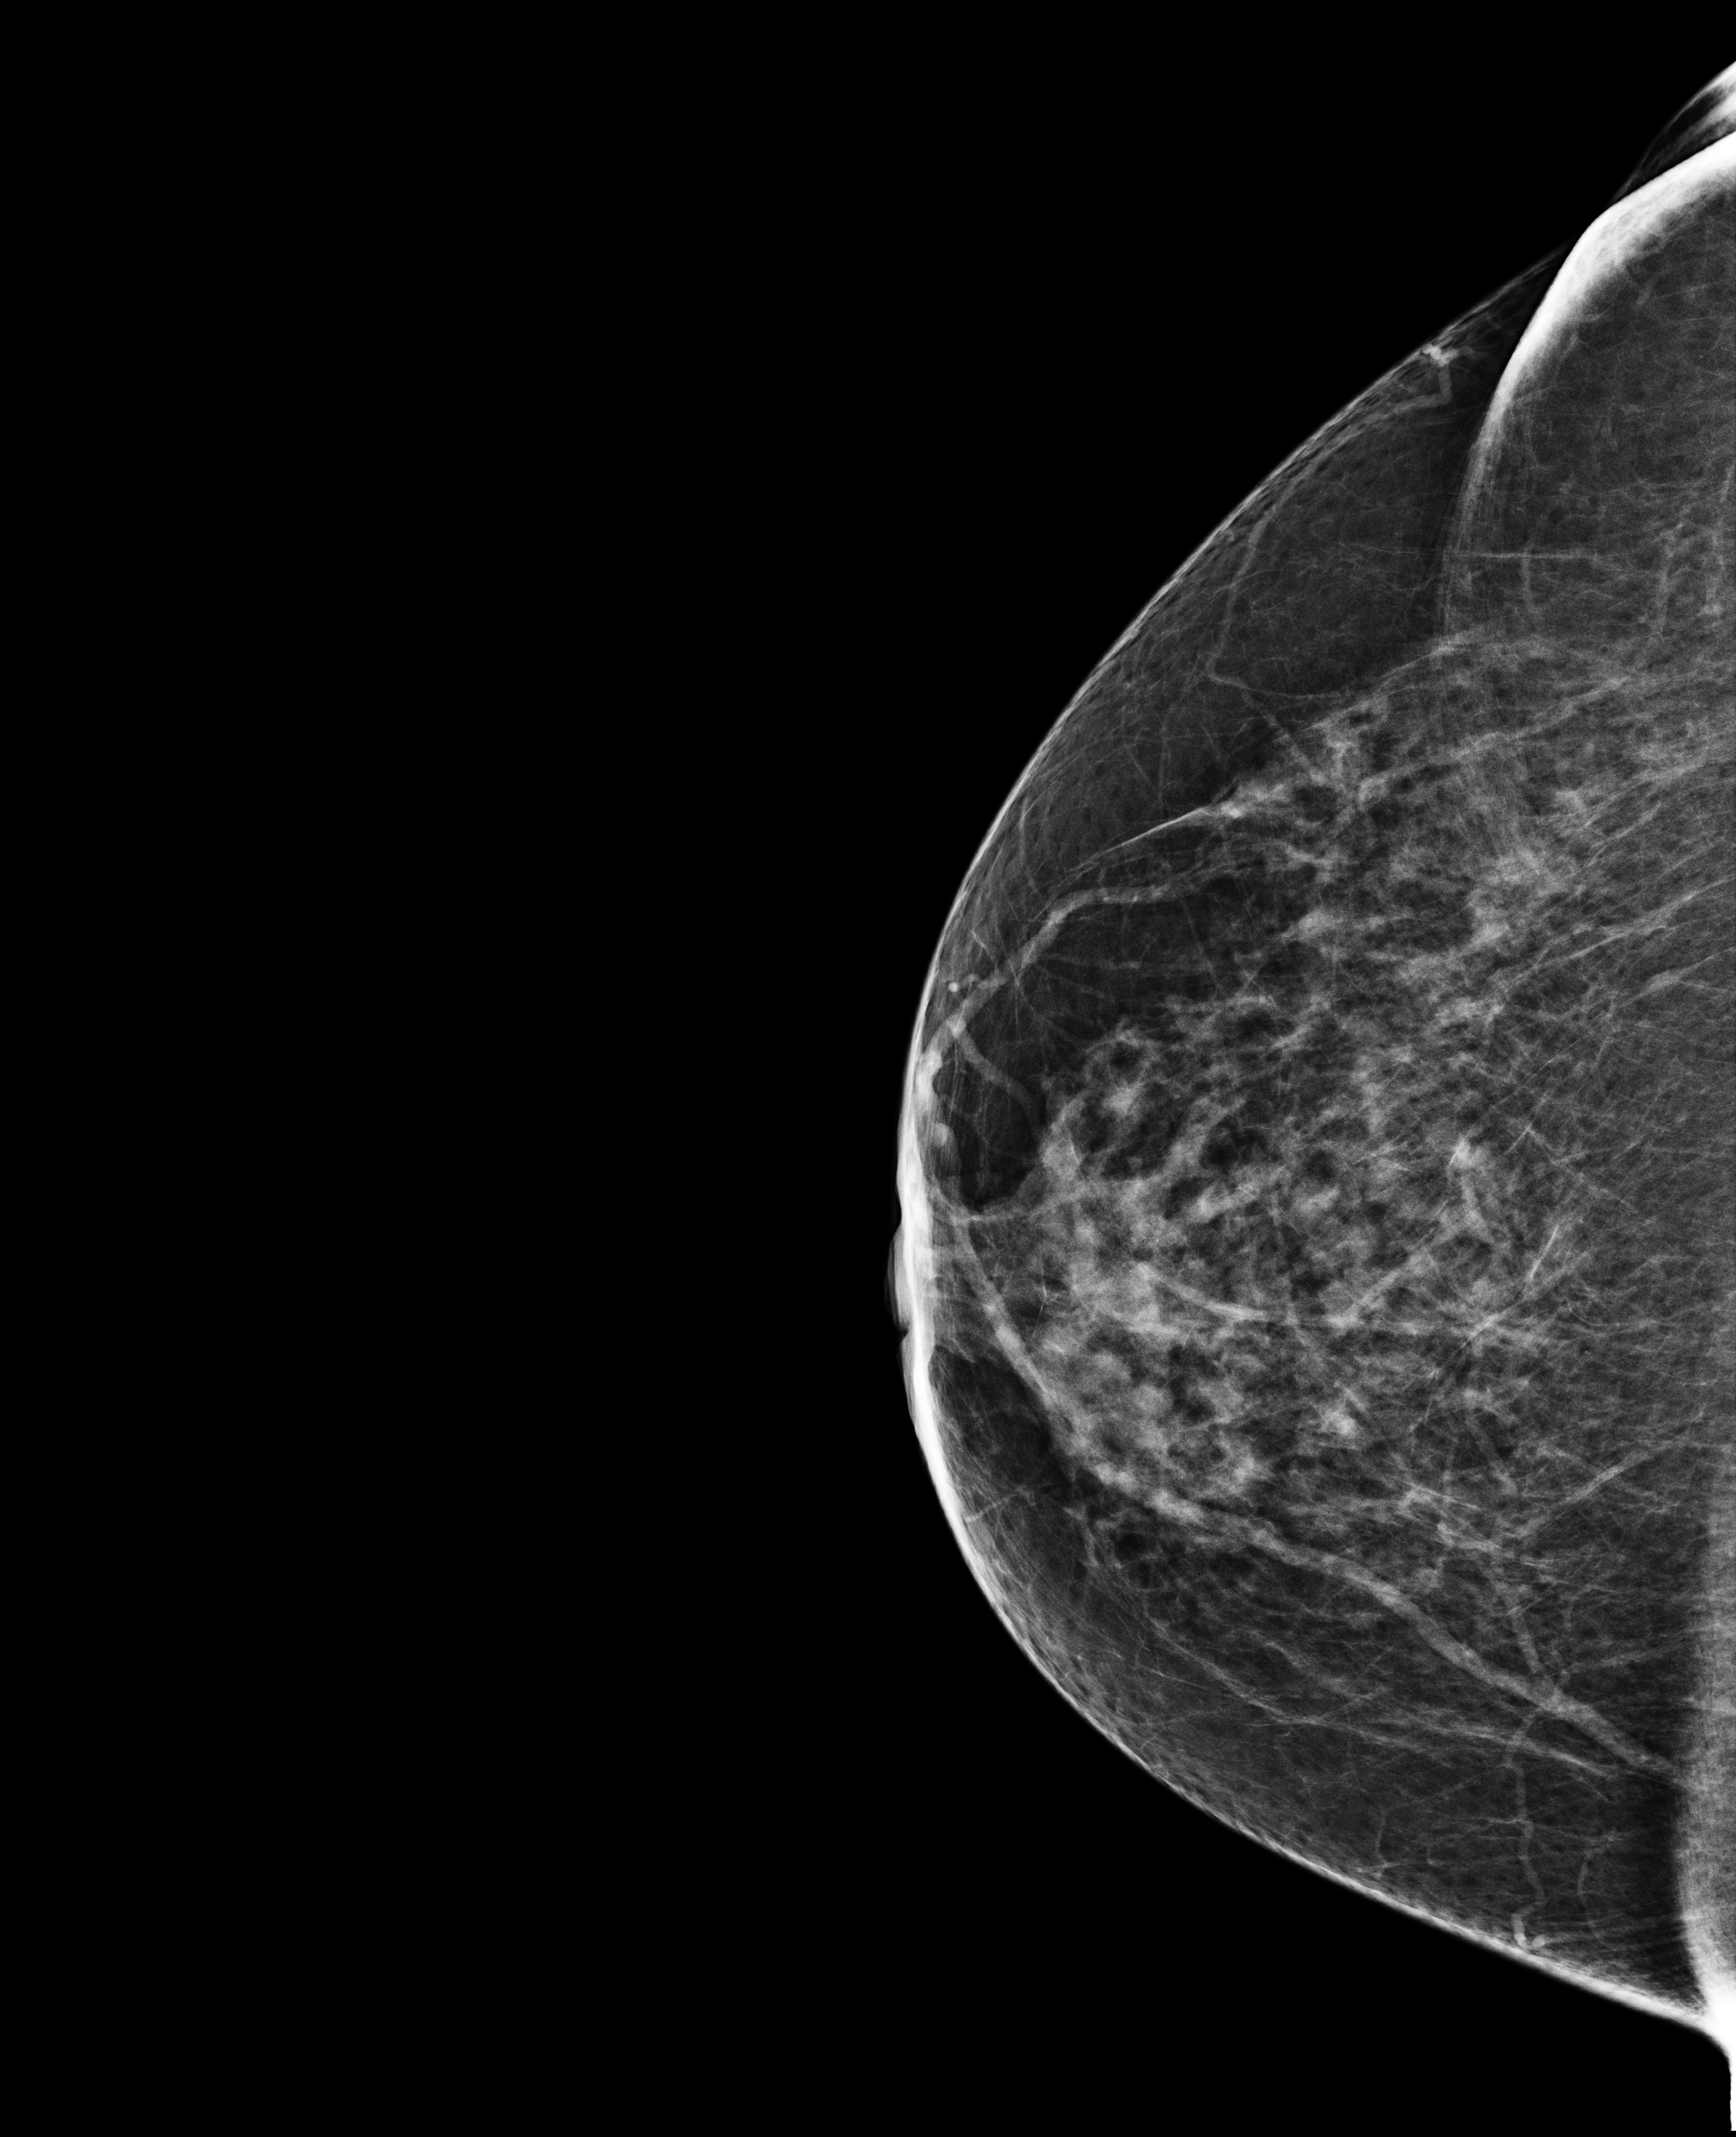
Screening examination; compressed breast thickness 50 mm. Female patient, age 72 years.
Image type: full-field digital mammogram. Breast: right. Projection: cranio-caudal projection.